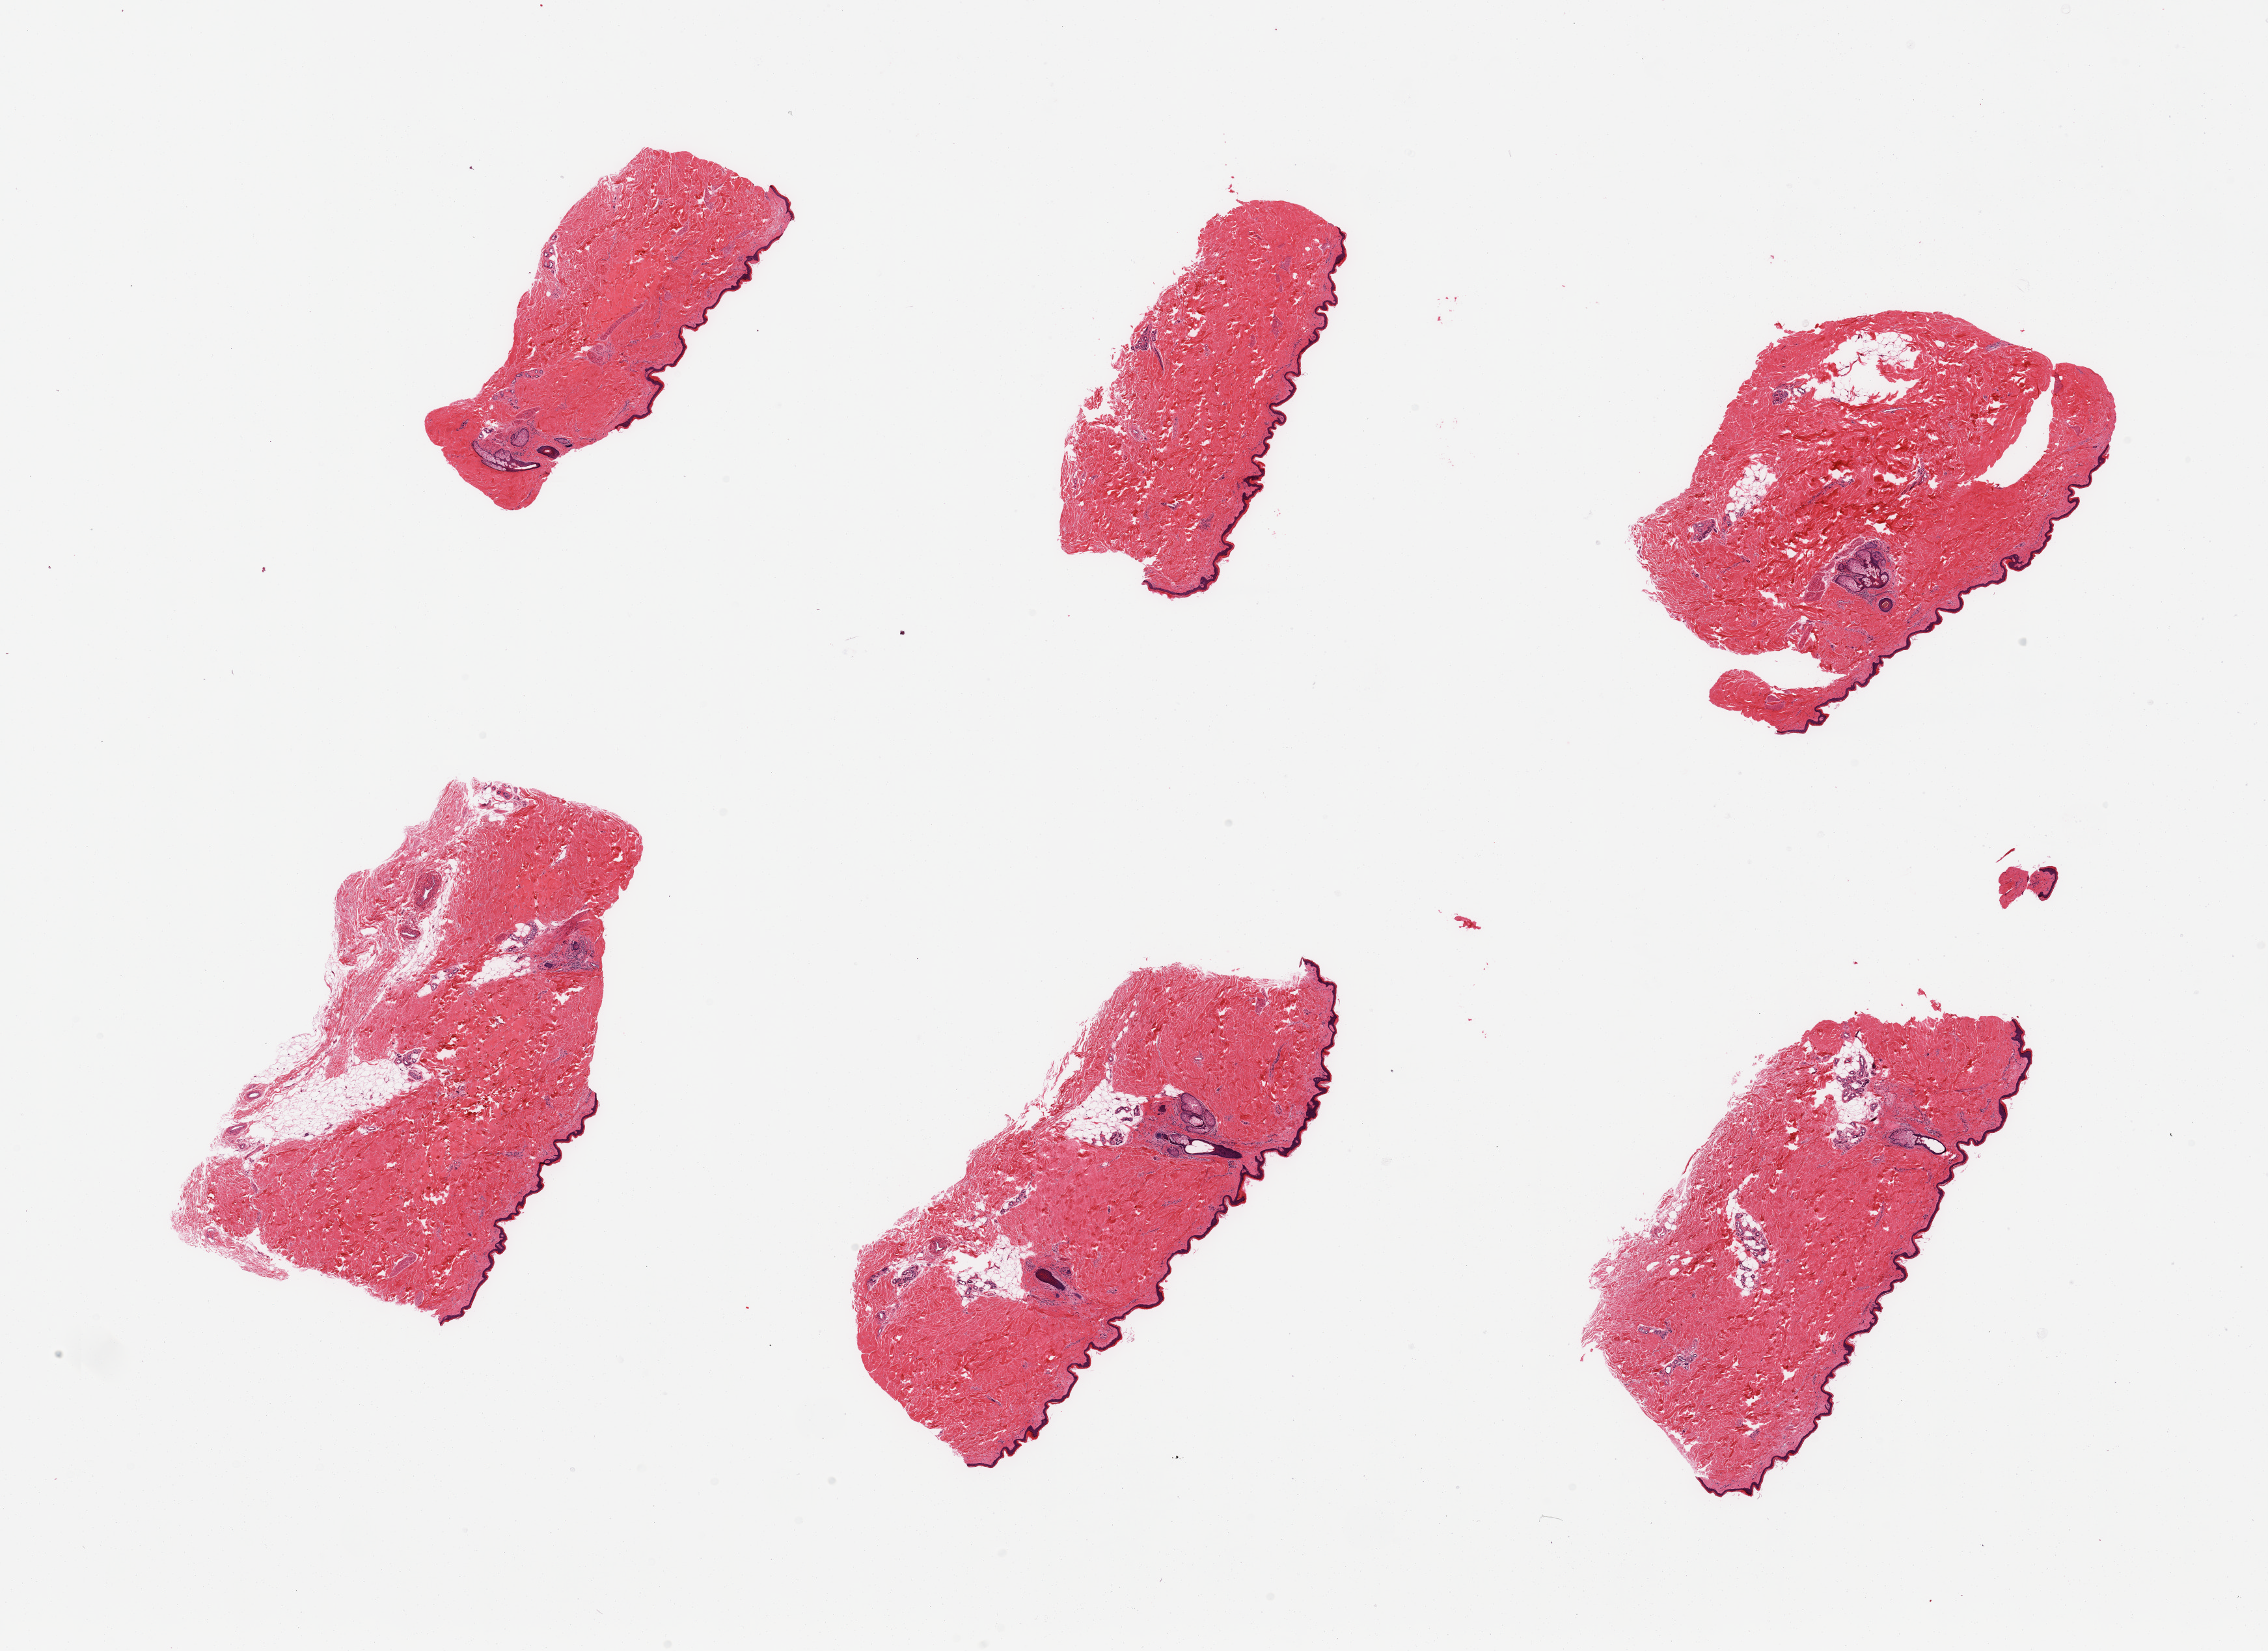
Hematoxylin and eosin (H&E) whole-slide image, whole scanned area (about 27.6 x 20.1 mm, slide scanned at 20x) shown as a low-resolution overview. PAXgene-fixed paraffin-embedded (PFPE) section. Section of skin of lower leg (target tissue). Tissue donor sample.
• pathologist's review note for this sample: 6 pieces; 10% intradermal fat